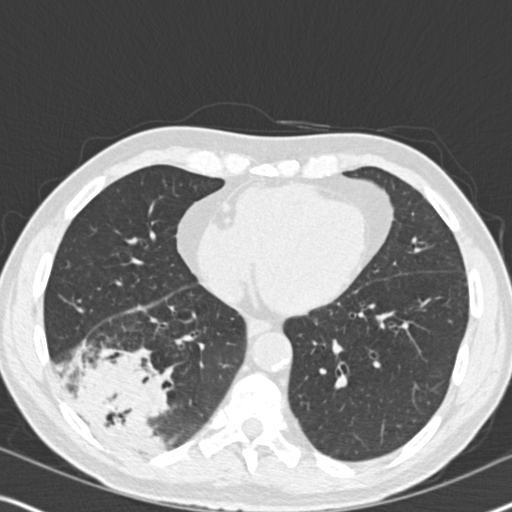
Low-dose screening chest CT, one axial slice; position 73 of 182 along the scan axis; lung window (W 1500 / L -600 HU); 512 × 512 image matrix.
Annotated regions visible in this slice (manually delineated by an expert):
- lesion 1 (tumor, lower lobe of right lung): box from (x=76, y=352) to (x=172, y=456) px